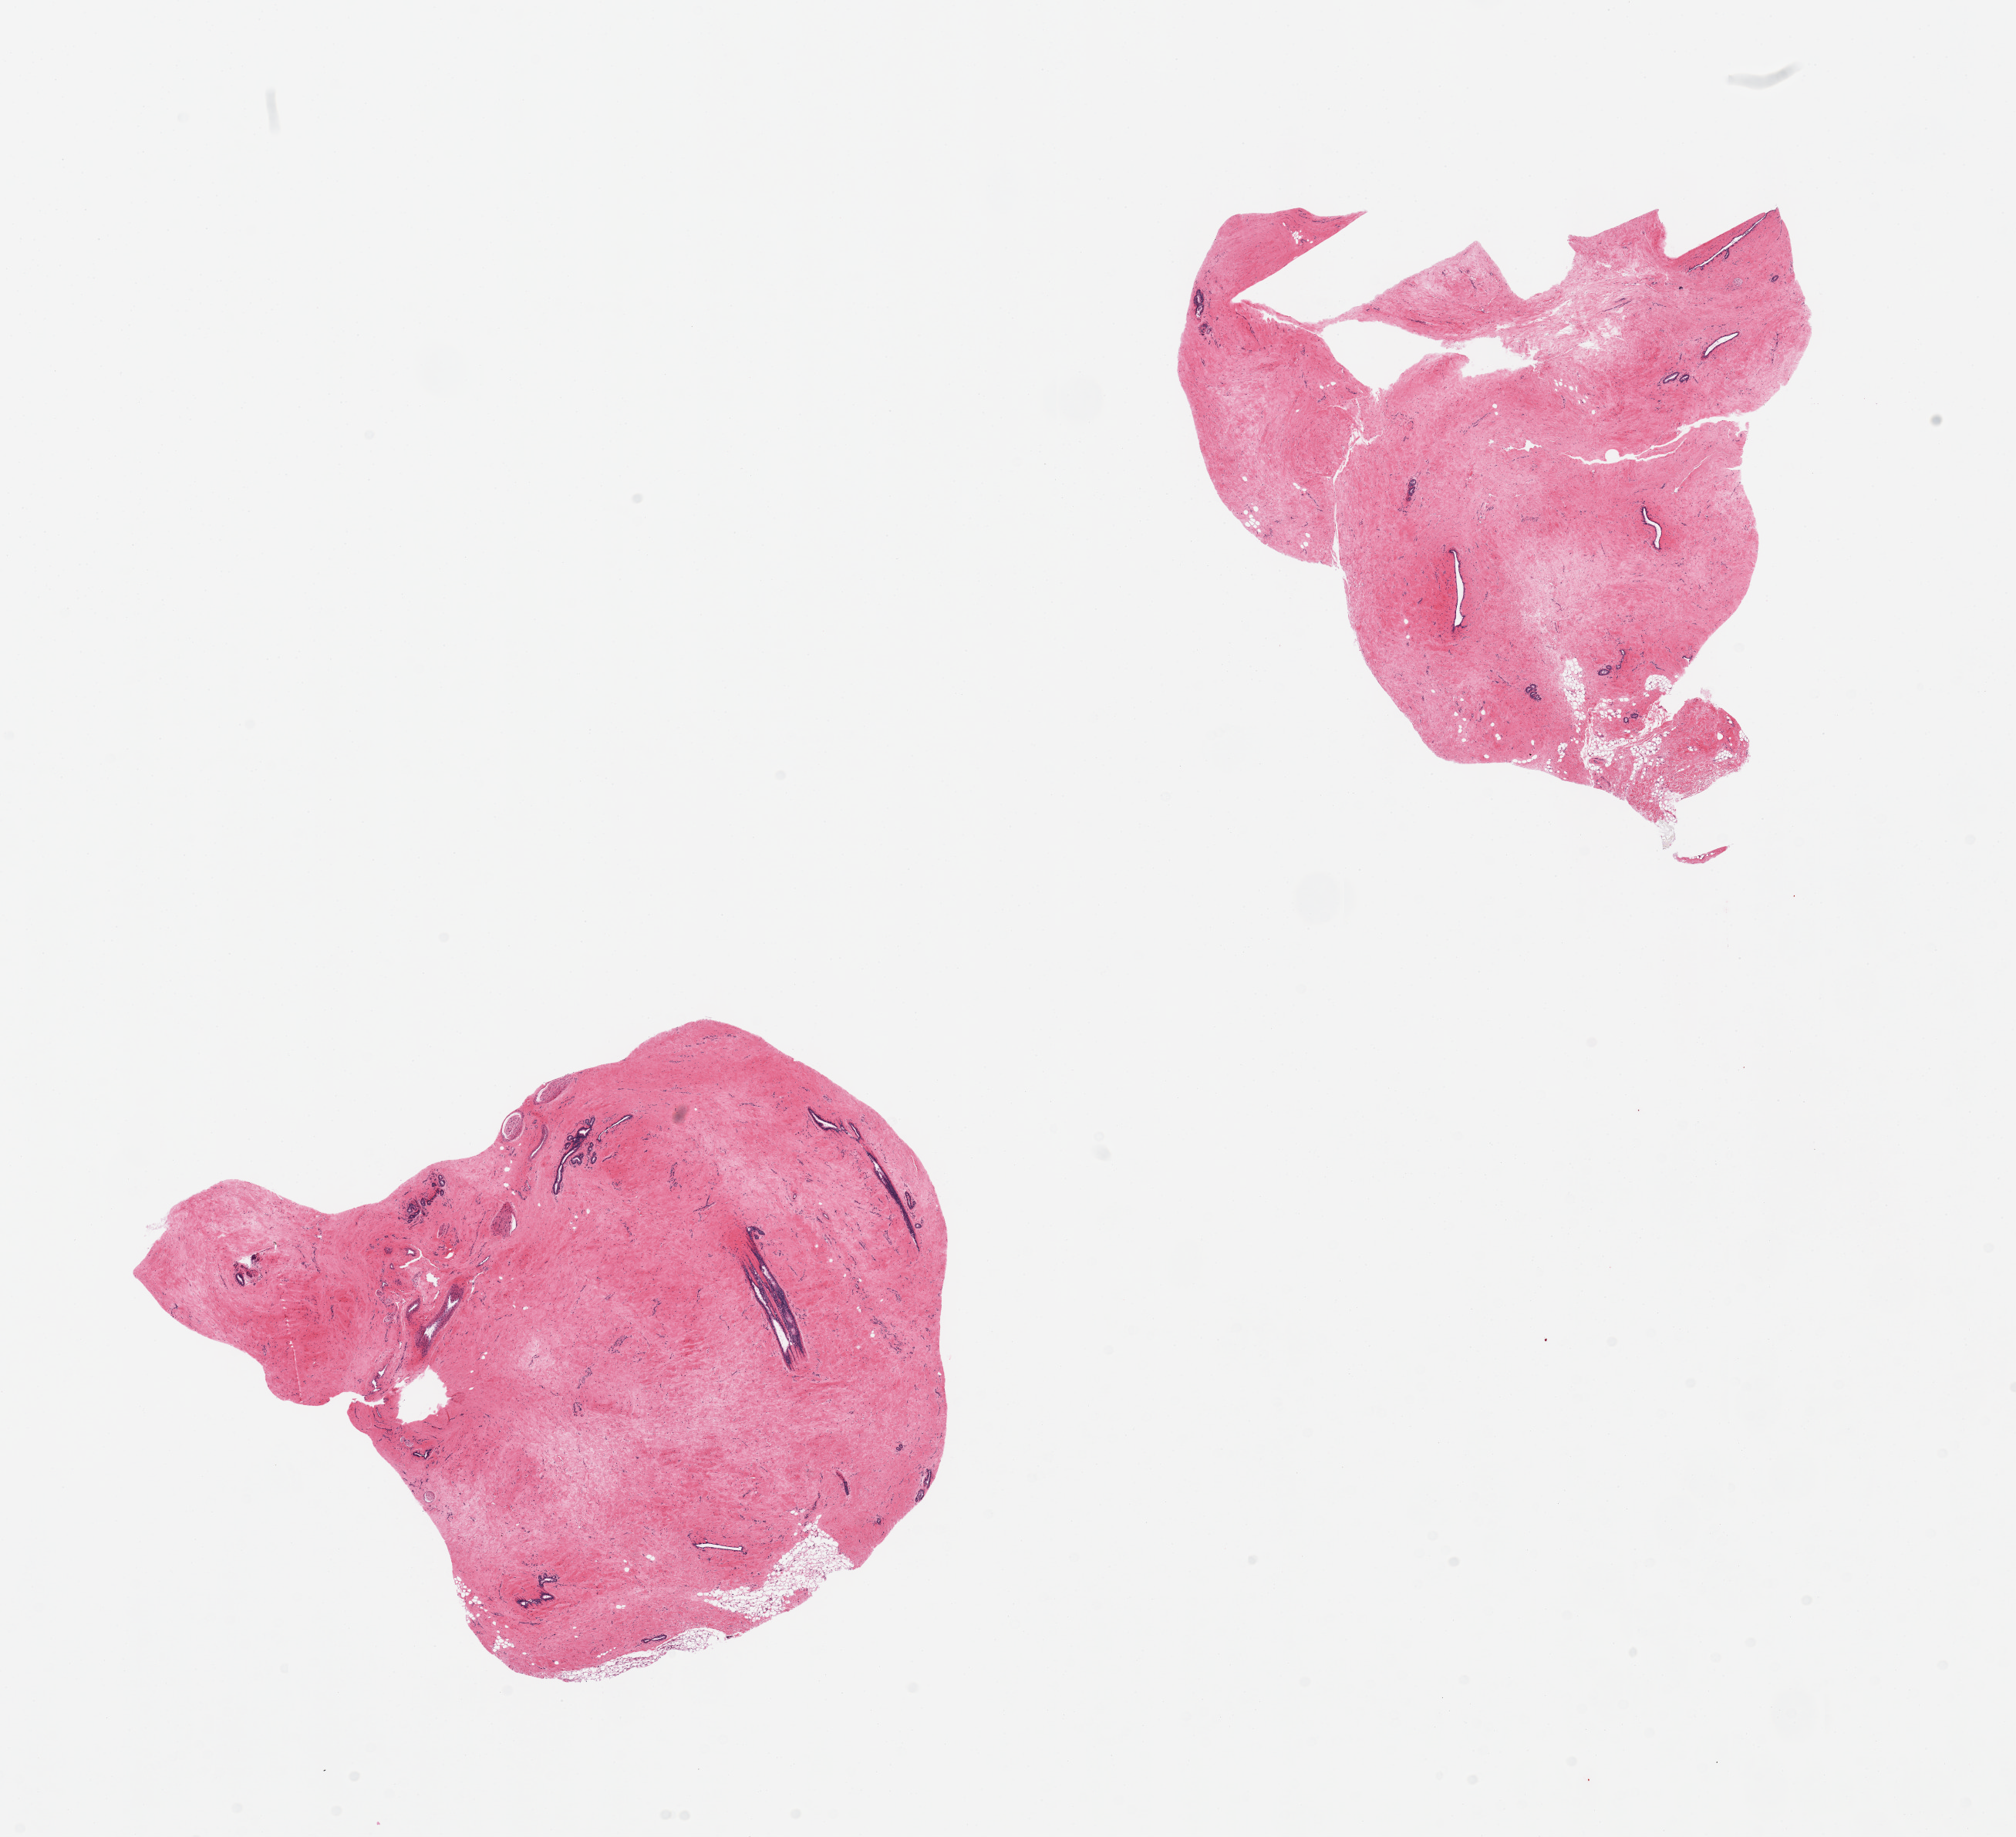
Whole-slide image, H&E stain — shown as a low-resolution overview of the whole scanned area (about 20.7 x 18.8 mm), PAXgene-fixed paraffin-embedded (PFPE) section, sampled site (target tissue): breast, donor tissue sample. Male donor.
* reviewer comment on this tissue sample: 2 pieces; stromal fibrosis & ducts: gynecomastoid hyperplasia